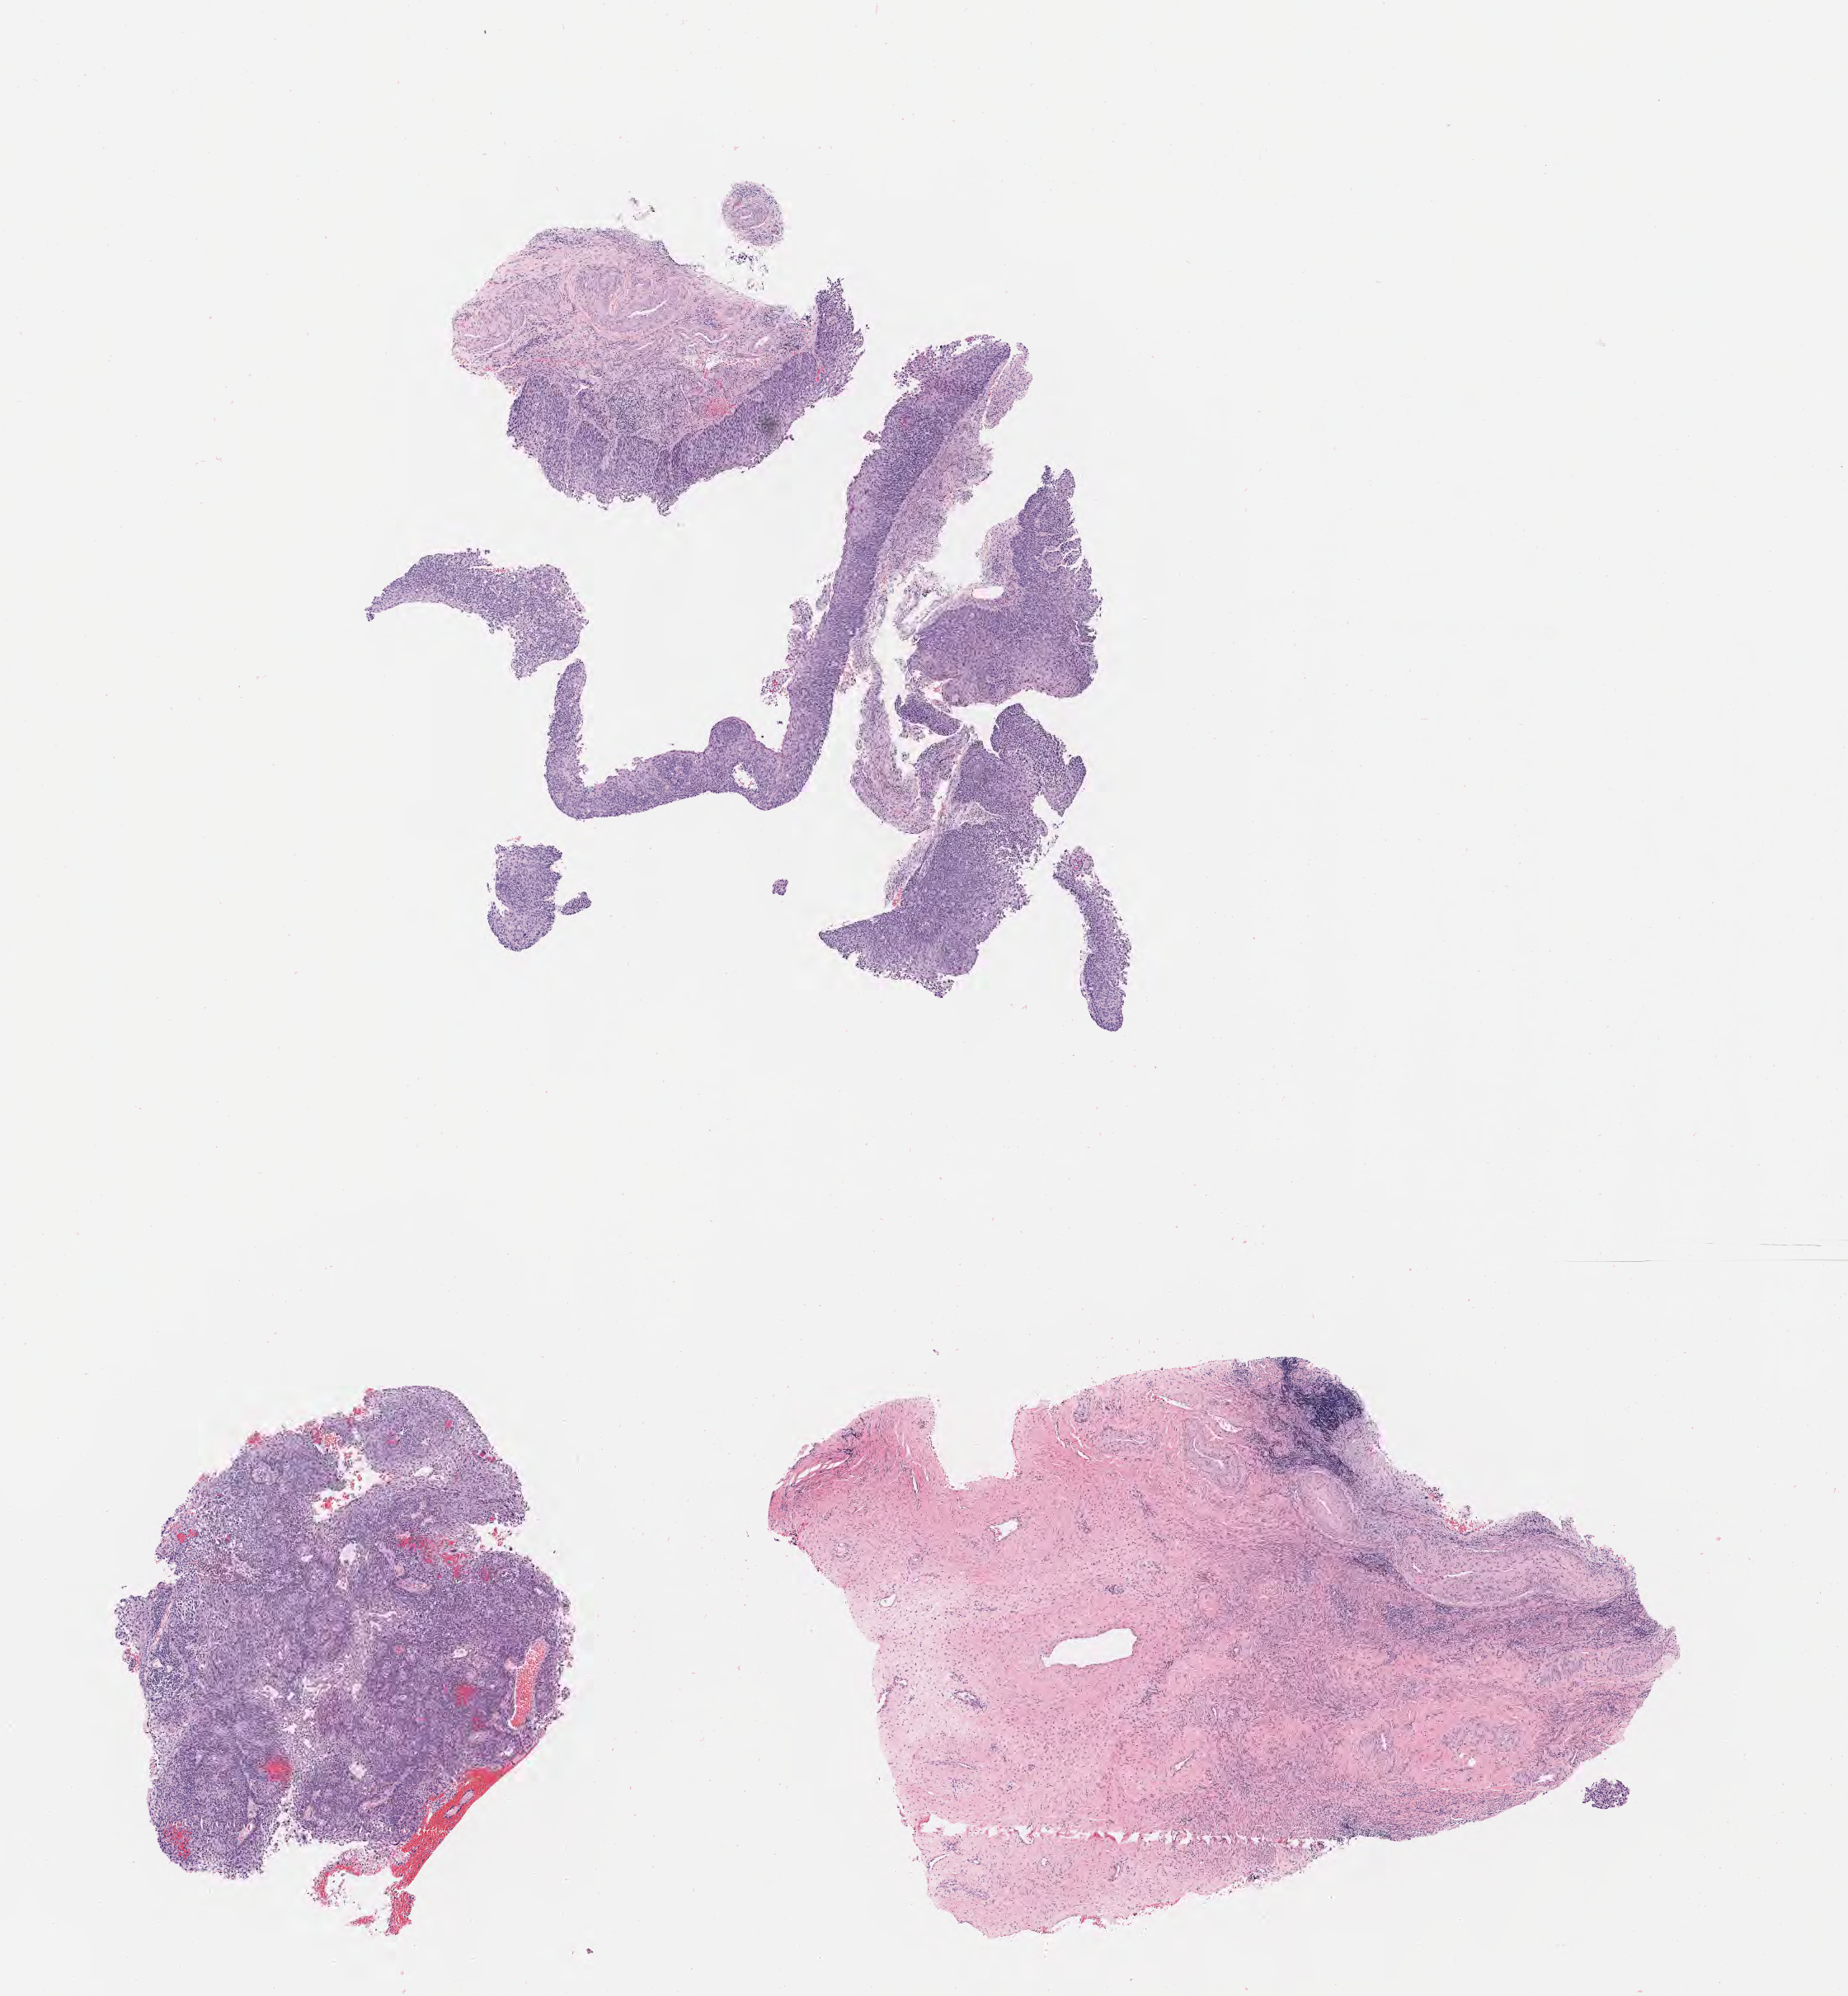
Whole-slide image, haematoxylin and eosin stain — whole scanned area (about 9.1 x 9.8 mm) shown as a low-resolution overview; specimen: tumor tissue; site: cervix. Patient: female, aged 60.
- histologic diagnosis: Squamous cell carcinoma, large cell, nonkeratinizing, NOS